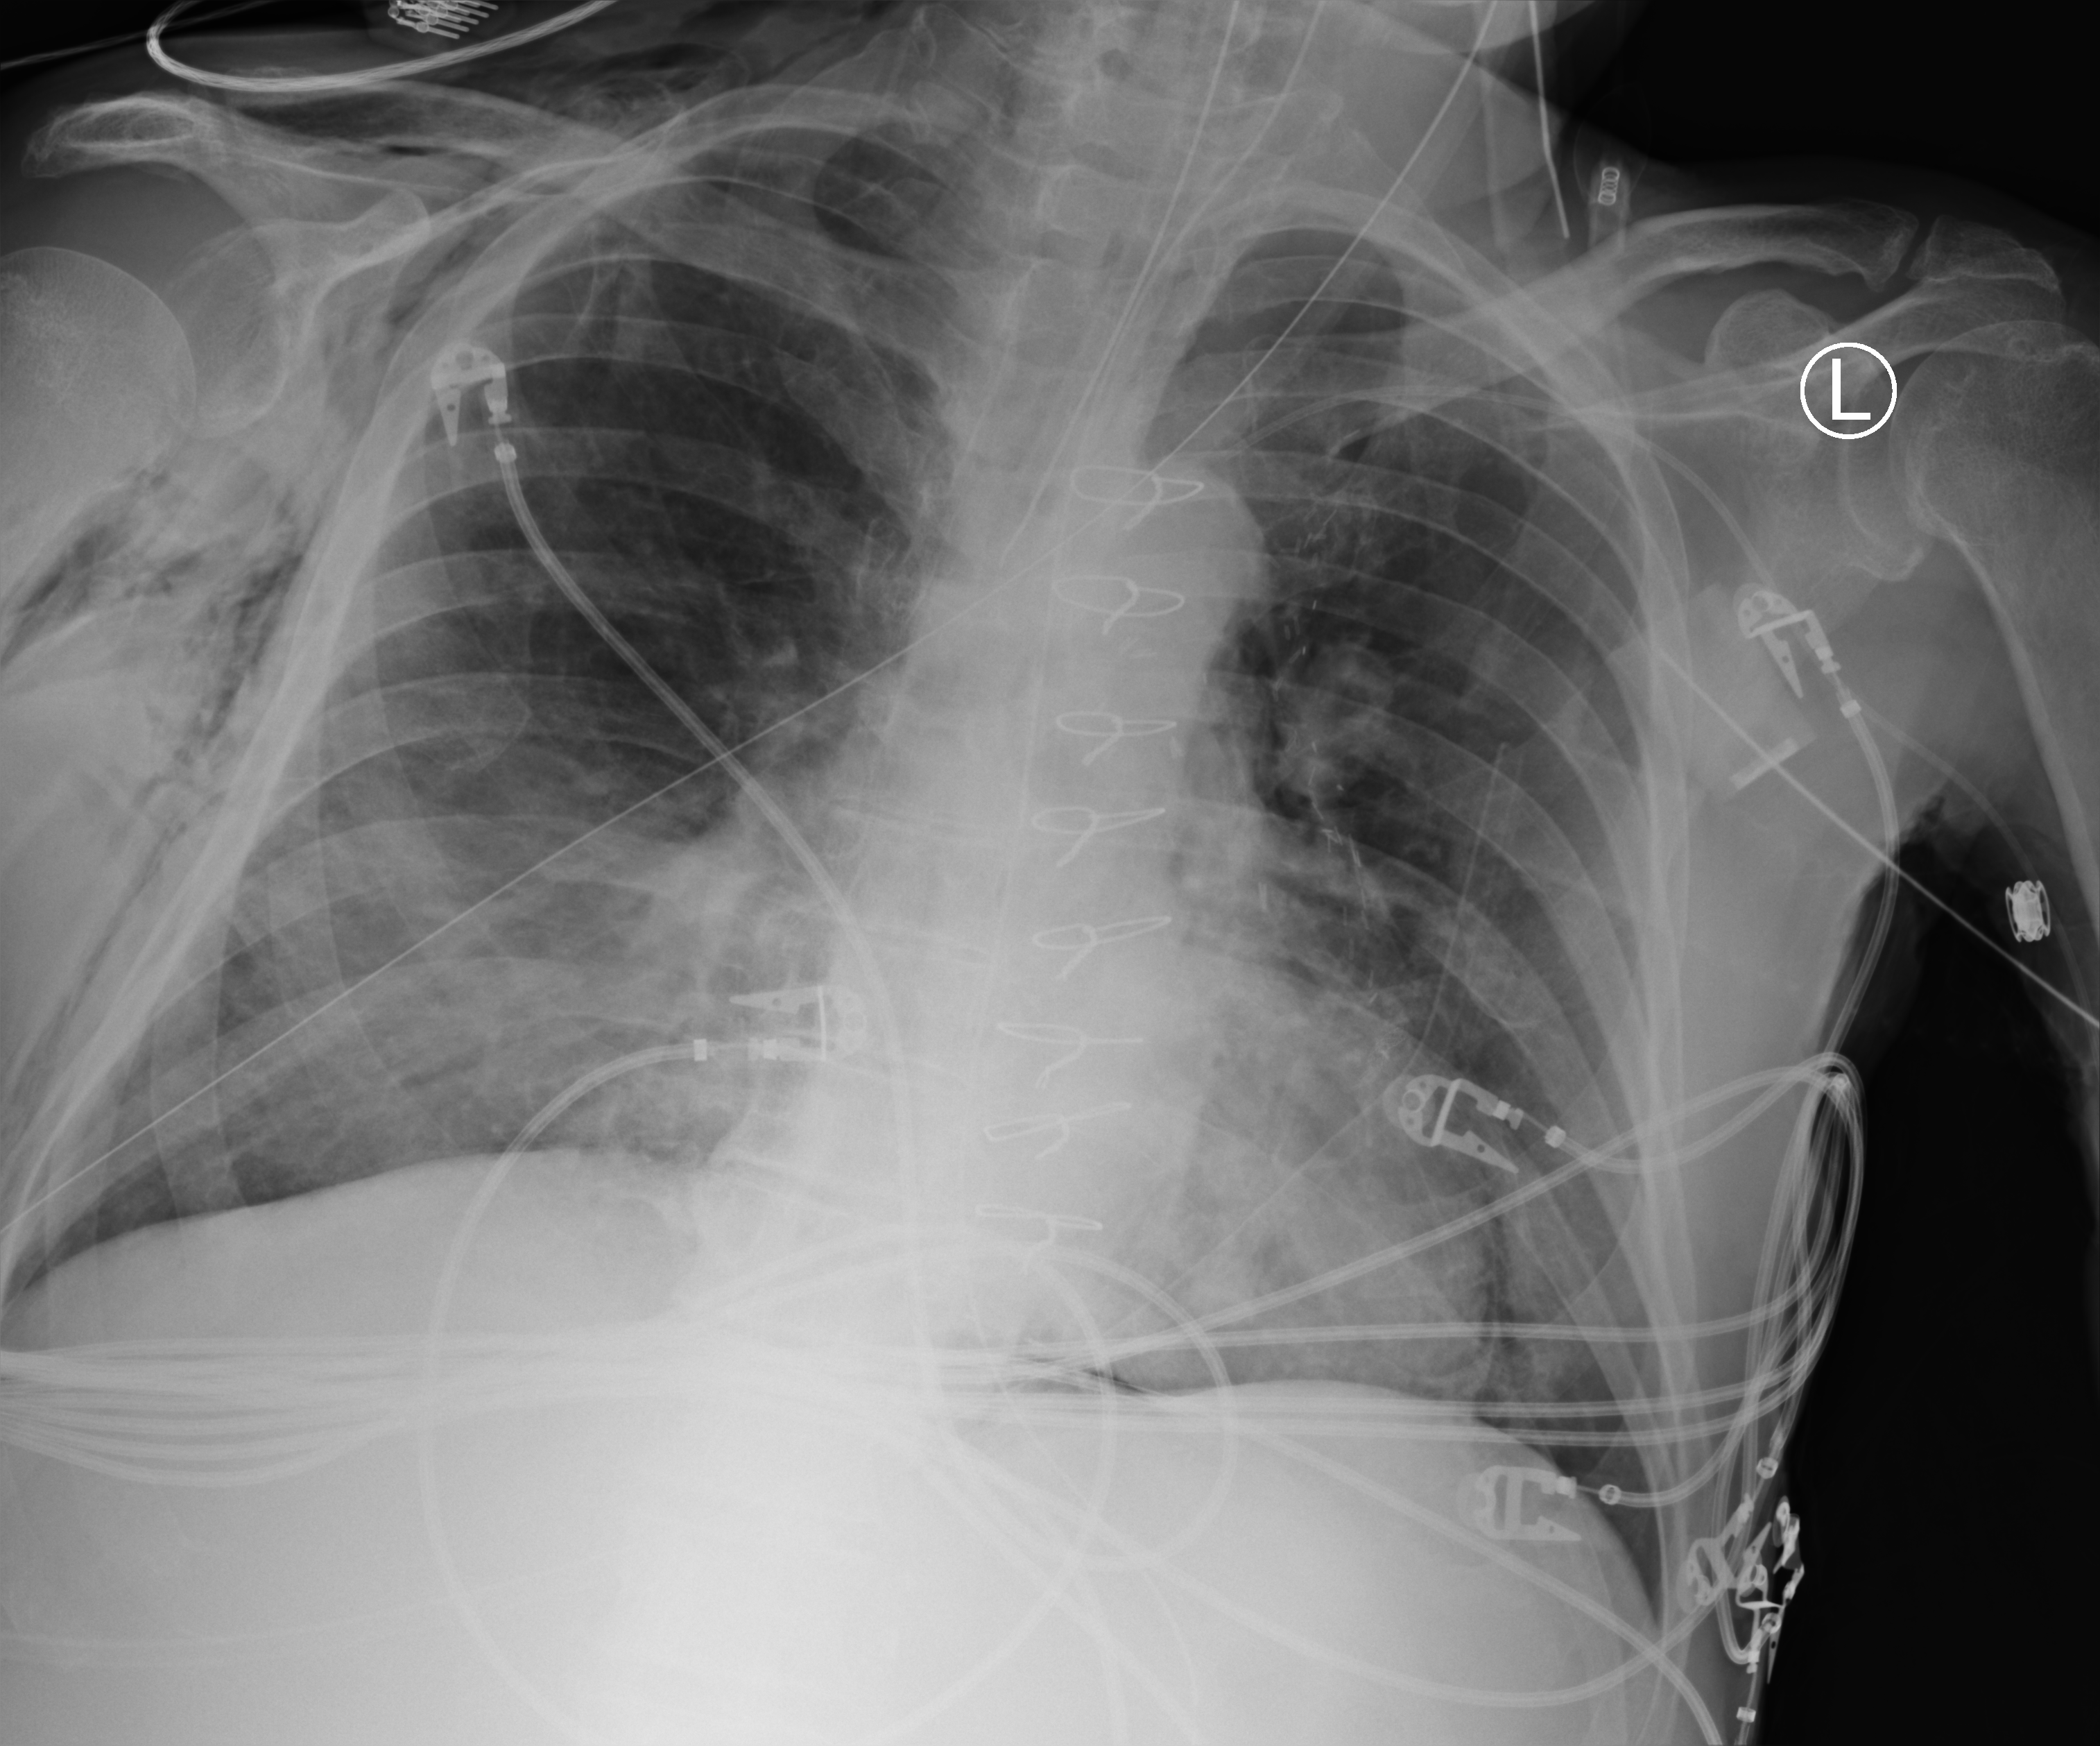
Bedside chest radiograph (computed radiography); anteroposterior (AP) projection. Patient hospitalised with COVID-19; male, aged 60–74 years.
From the hospital-stay record, not from the radiograph (when in the stay this image was taken is not recorded): admitted to intensive care during this hospital stay: yes.